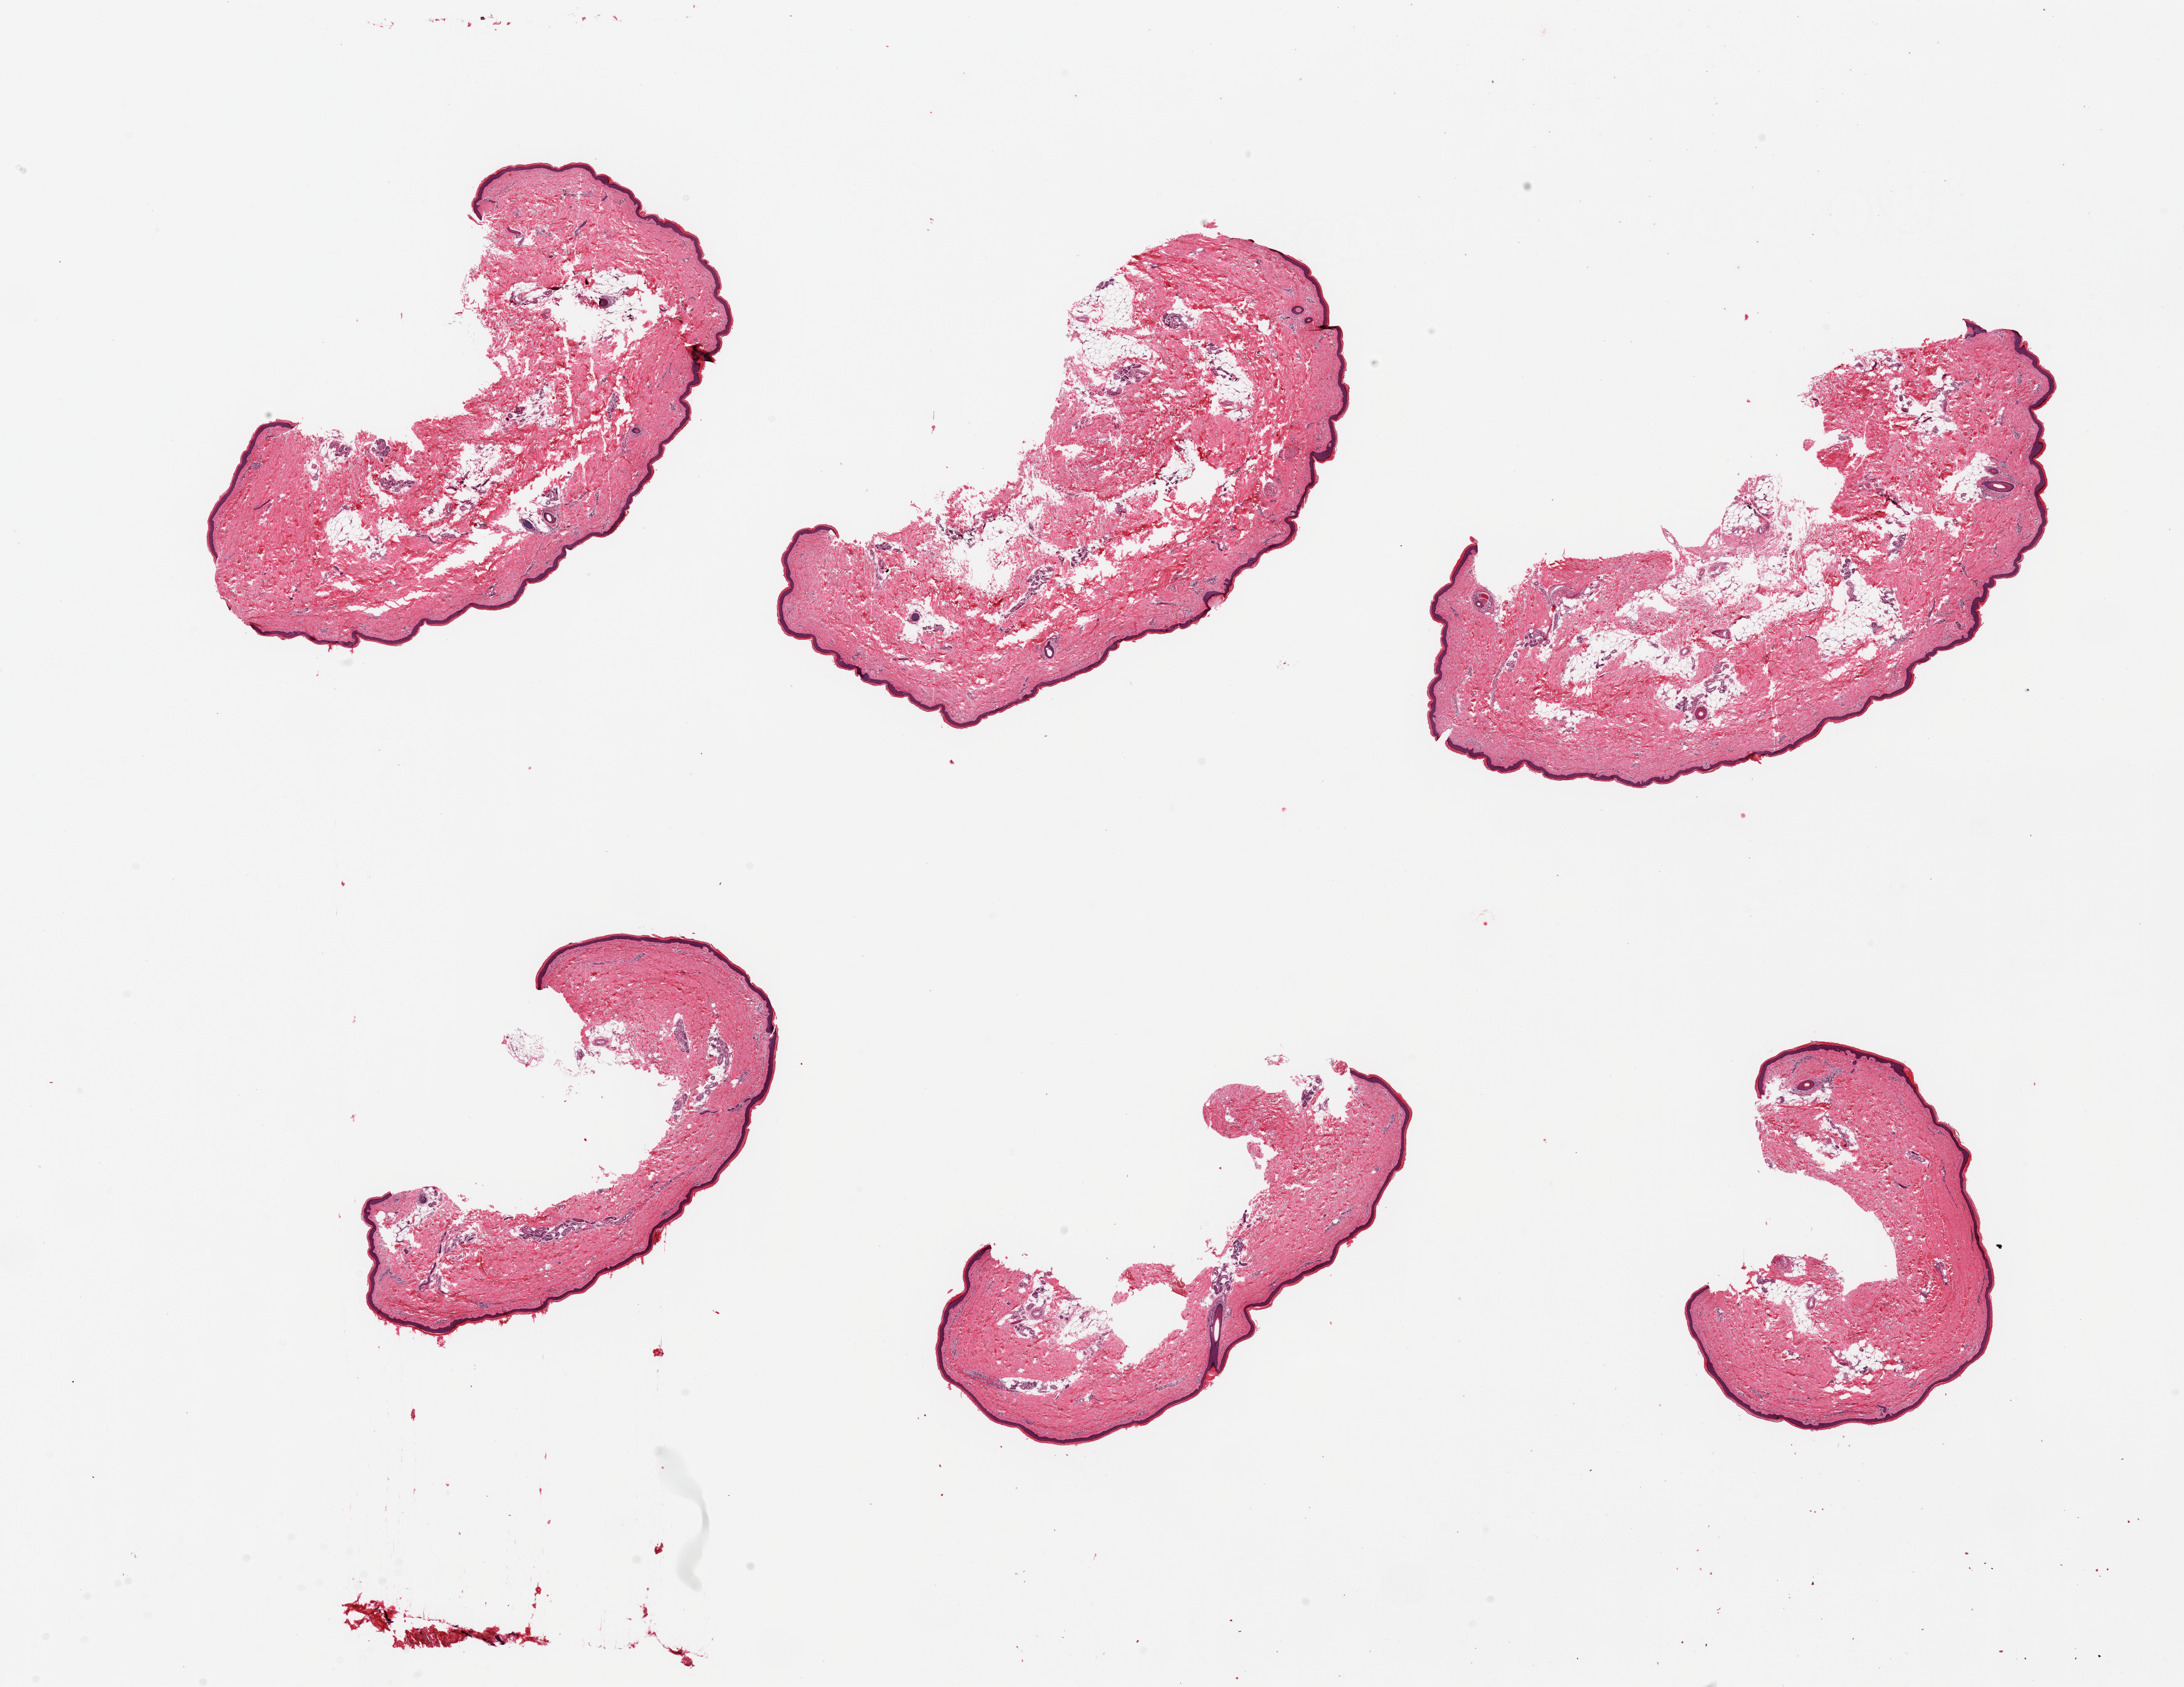
Digitized hematoxylin and eosin (H&E)-stained section — low-resolution overview of the scanned area, about 27.6 x 21.3 mm (from a 20x scan); PAXgene-fixed, paraffin-embedded tissue; target tissue: skin of lower leg; donor tissue sample. Donor: female.
* review note (as recorded): 6 pieces; well trimmed; fragmented dermis; 3 have 20% dermal fat; 3 have 10% dermal fat